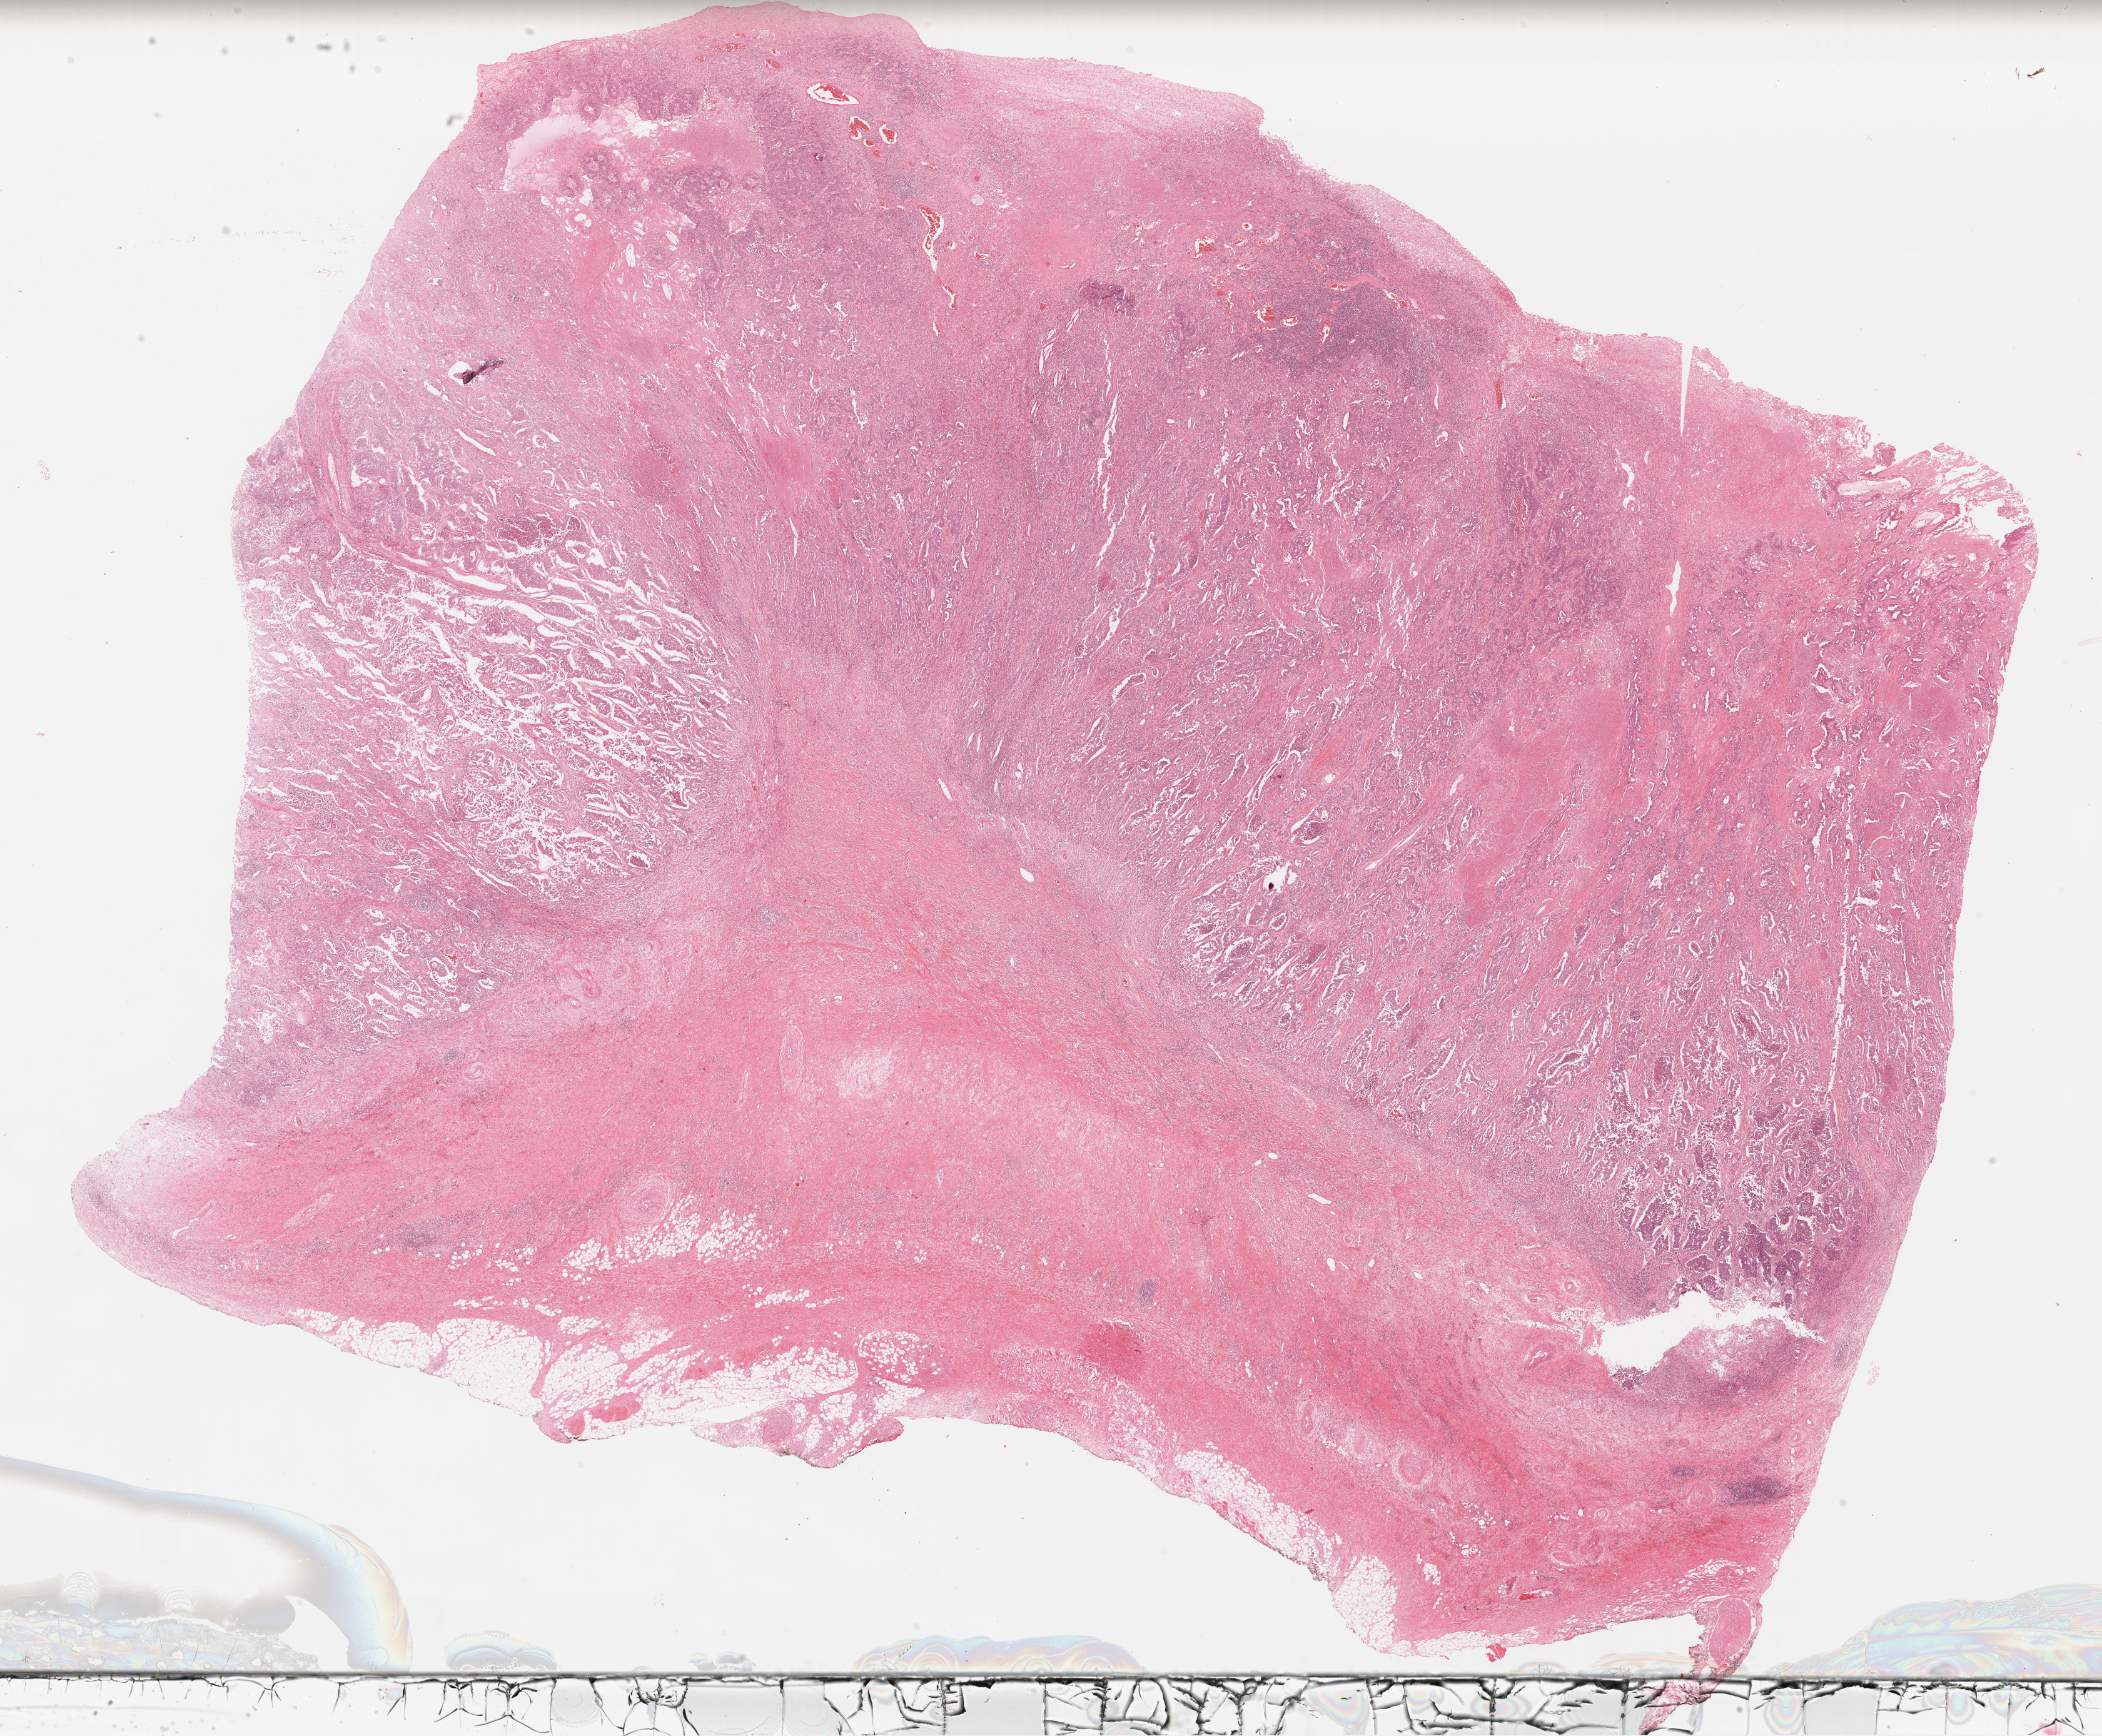
Digitized Hematoxylin and eosin (H&E) stained tissue section (whole slide) — a low-resolution overview of the entire scanned area, about 26.4 x 21.8 mm, FFPE section, primary tumour sample from the lung. Female patient; age at initial diagnosis 58 years.
AJCC pathologic stage: IIB (6th edition). TNM: T3 N0 M0. Laterality: right. Pathologic diagnosis: Adenocarcinoma, NOS (upper lobe, lung).